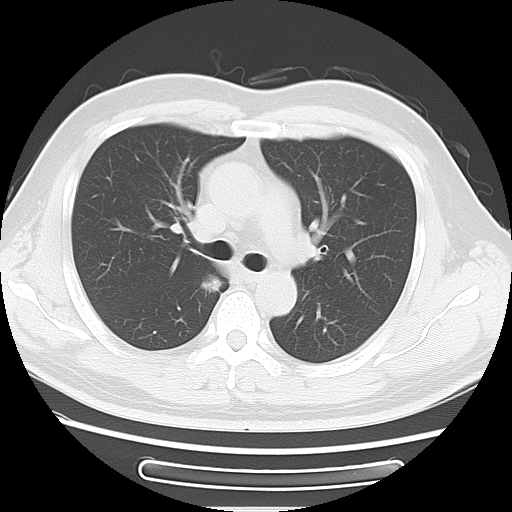
Chest CT, one axial slice. Reconstruction kernel LUNG. 120 kVp. Lung window (W 1500 / L -600 HU). 5 mm slice thickness. 512 × 512 image matrix, field of view 350 × 350 mm. Patient: male, 49 years. Case-level facts recorded for this patient, not image findings: clinical TNM (as recorded): T1b N0 M0.
Structures marked on this image (rectangle marked by the reading radiologist):
- lung tumour (recorded histology: adenocarcinoma): box from (x=199, y=270) to (x=225, y=298) px